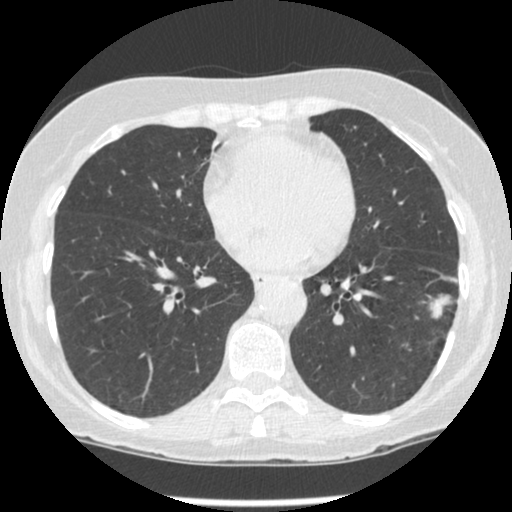
Low-dose screening chest CT, one axial slice; reconstruction kernel STANDARD; lung window (W 1500 / L -600 HU); 512 × 512 image matrix, field of view 303 × 303 mm.
Annotated regions visible in this slice (manually delineated by an expert):
- lesion 1 (tumor, lower lobe of left lung): box from (x=429, y=295) to (x=452, y=319) px